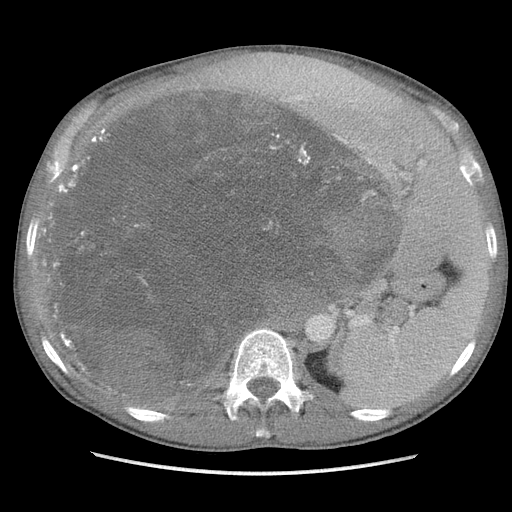
Contrast-enhanced abdominal CT, one axial slice; position 71 of 115 along the scan axis; soft-tissue window (W 400 / L 40 HU); 5 mm slice thickness; 512 × 512 image matrix, field of view 360 × 360 mm. Male patient. Case-level facts recorded for this patient, not image findings: diagnosis: adrenocortical carcinoma; tumour side: right adrenal; Ki-67 index: 13 %; stage (as recorded): 3.
Structures marked on this image (semi-automatically segmented with operator editing):
- mass: box from (x=52, y=93) to (x=391, y=388) px